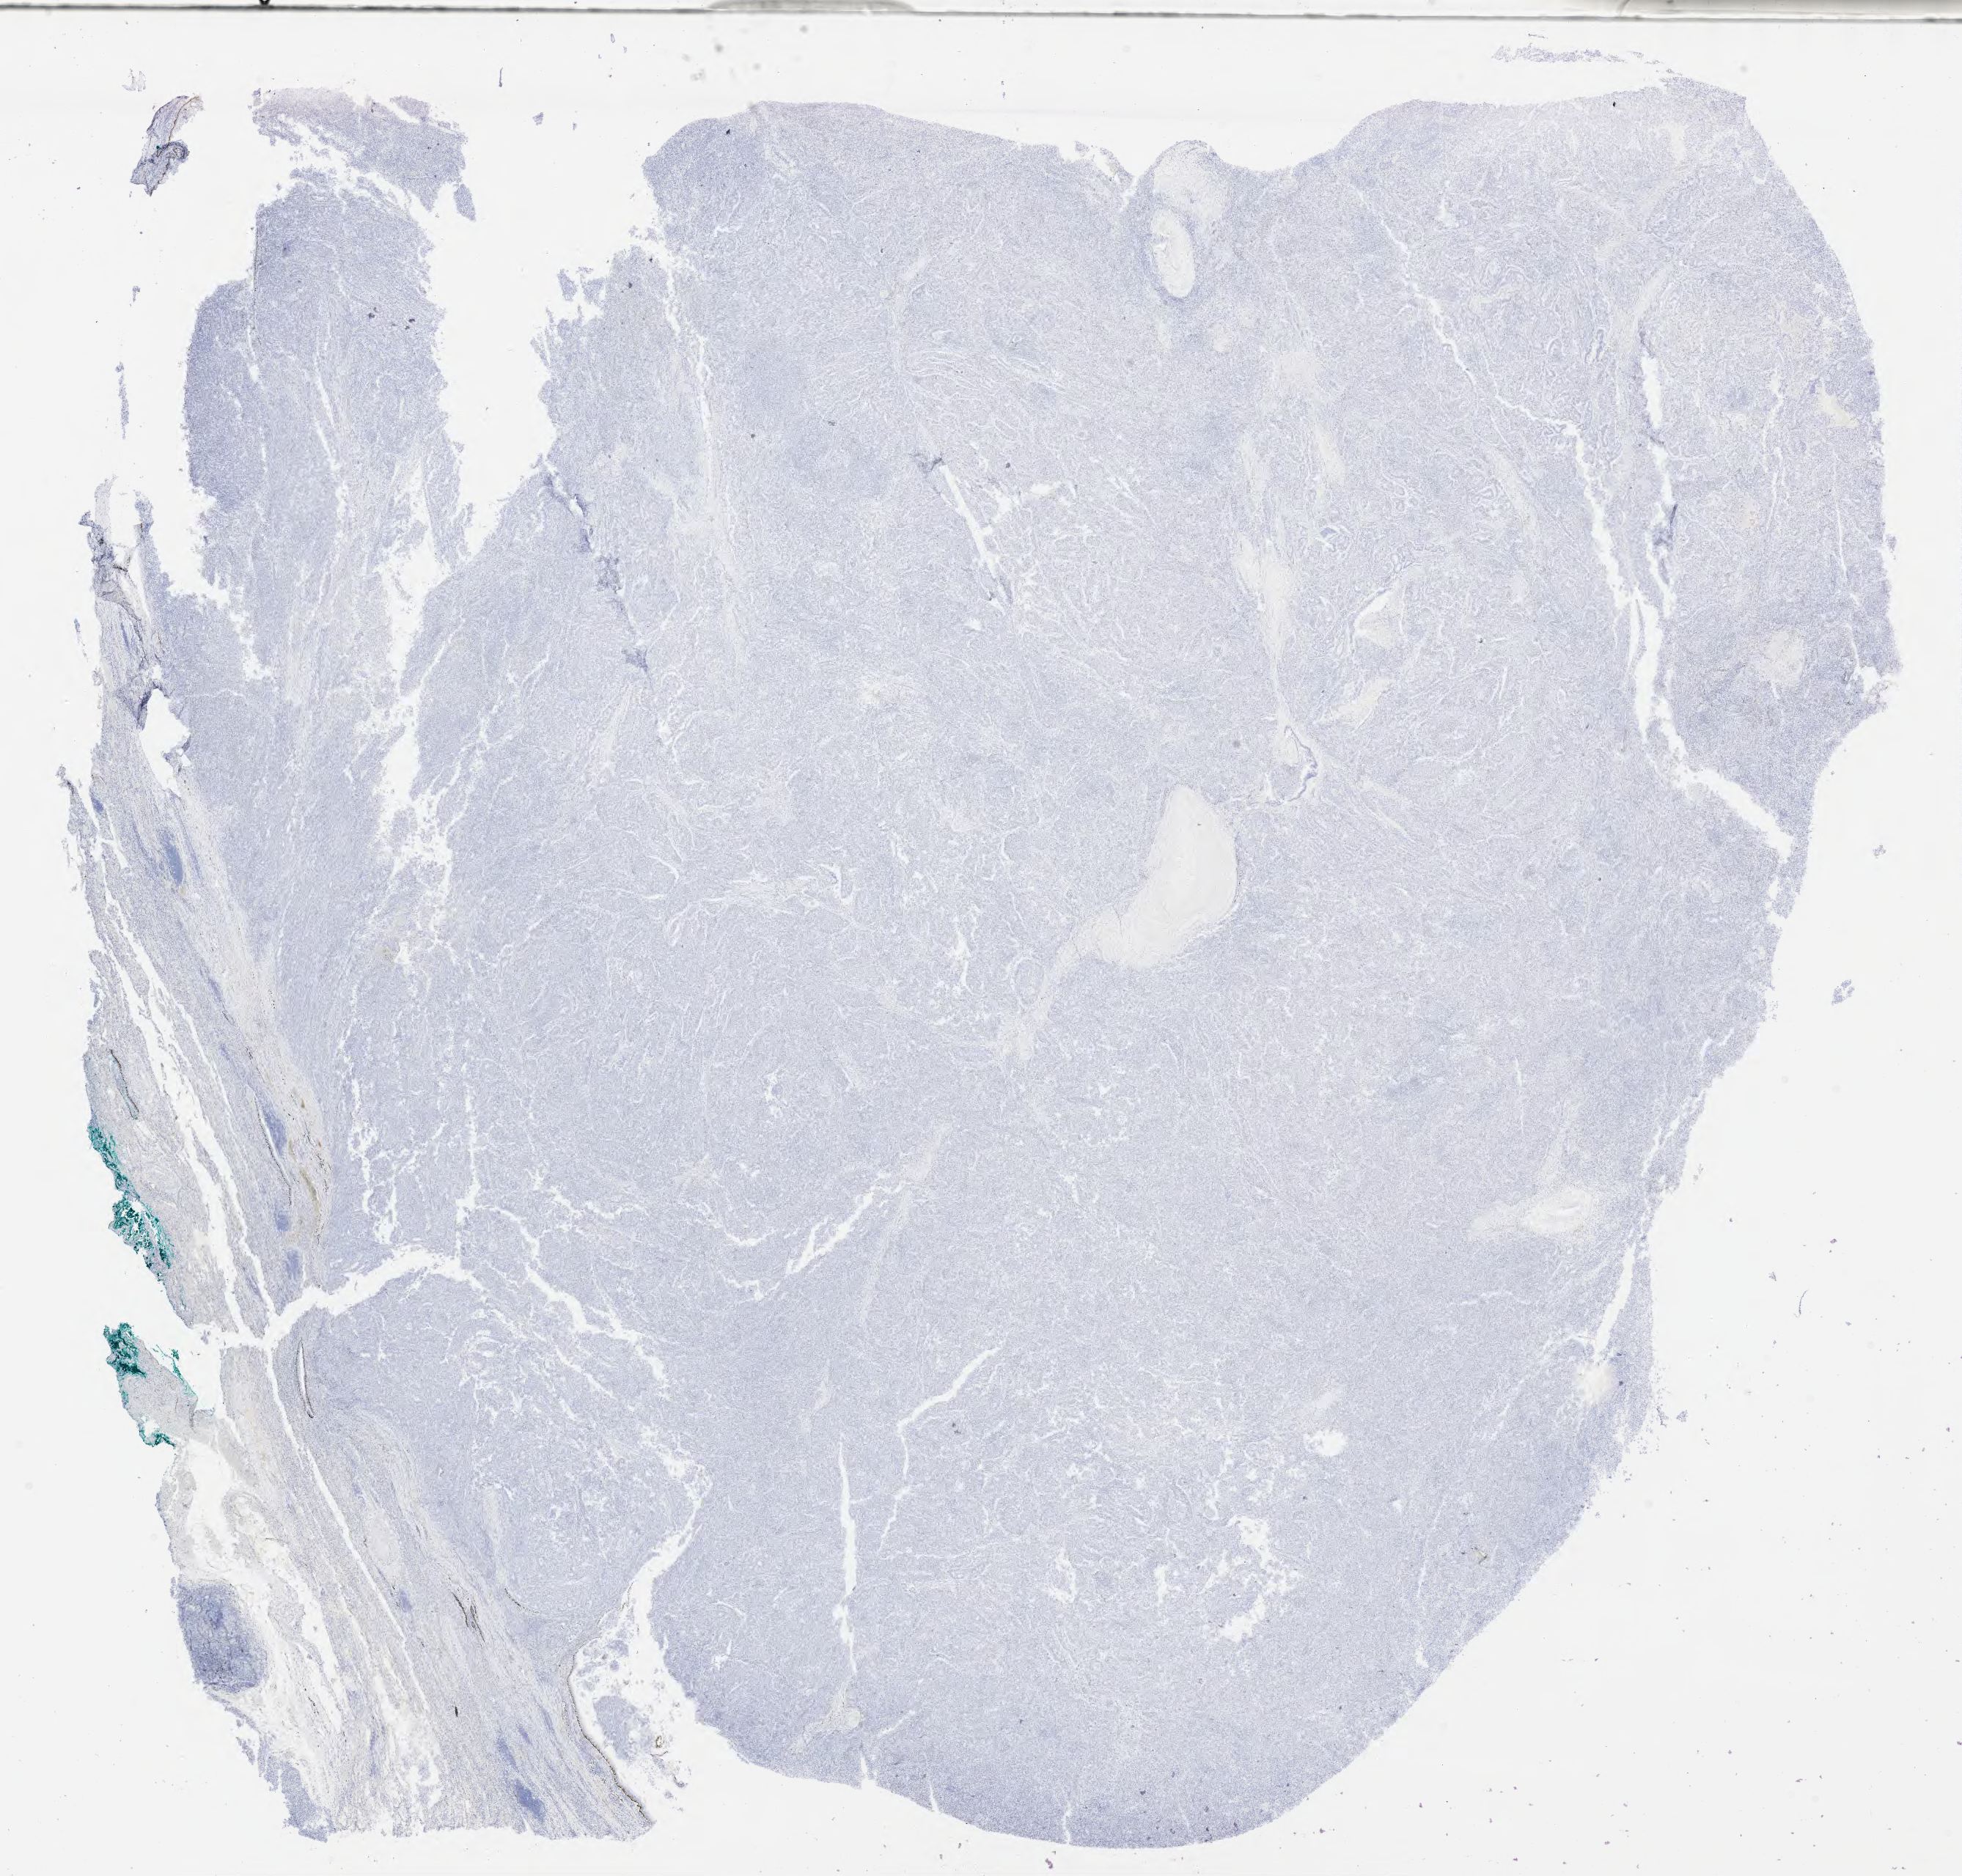
Whole-slide image, immunohistochemical stain for p40, shown as a low-resolution overview of the whole scanned area (about 21.6 x 20.7 mm). Specimen: tumor tissue. Site: lung. Patient male; aged 52.
Diagnosis: Non-small cell carcinoma.